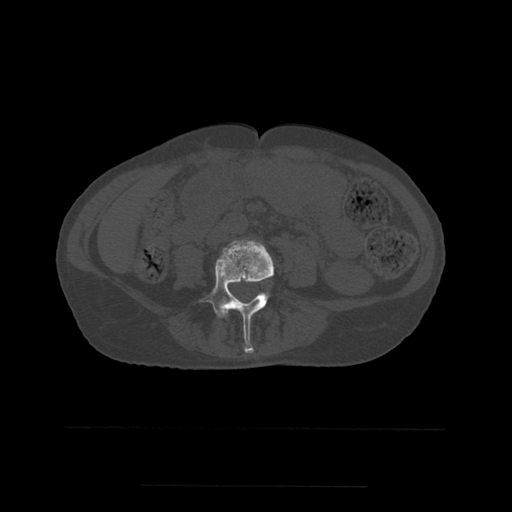
CT including the spine, one axial slice. Position 167 of 544 along the scan axis. Bone window (W 1800 / L 400 HU). 1.25 mm slice thickness. 512 × 512 image matrix. Patient age 58 years. Case-level facts recorded for this patient, not image findings: primary cancer: lung.
Outlined on this slice (semi-automatically segmented with operator editing):
- L4 vertebra: bounding box <202,240,274,354> (left, top, right, bottom; pixels)